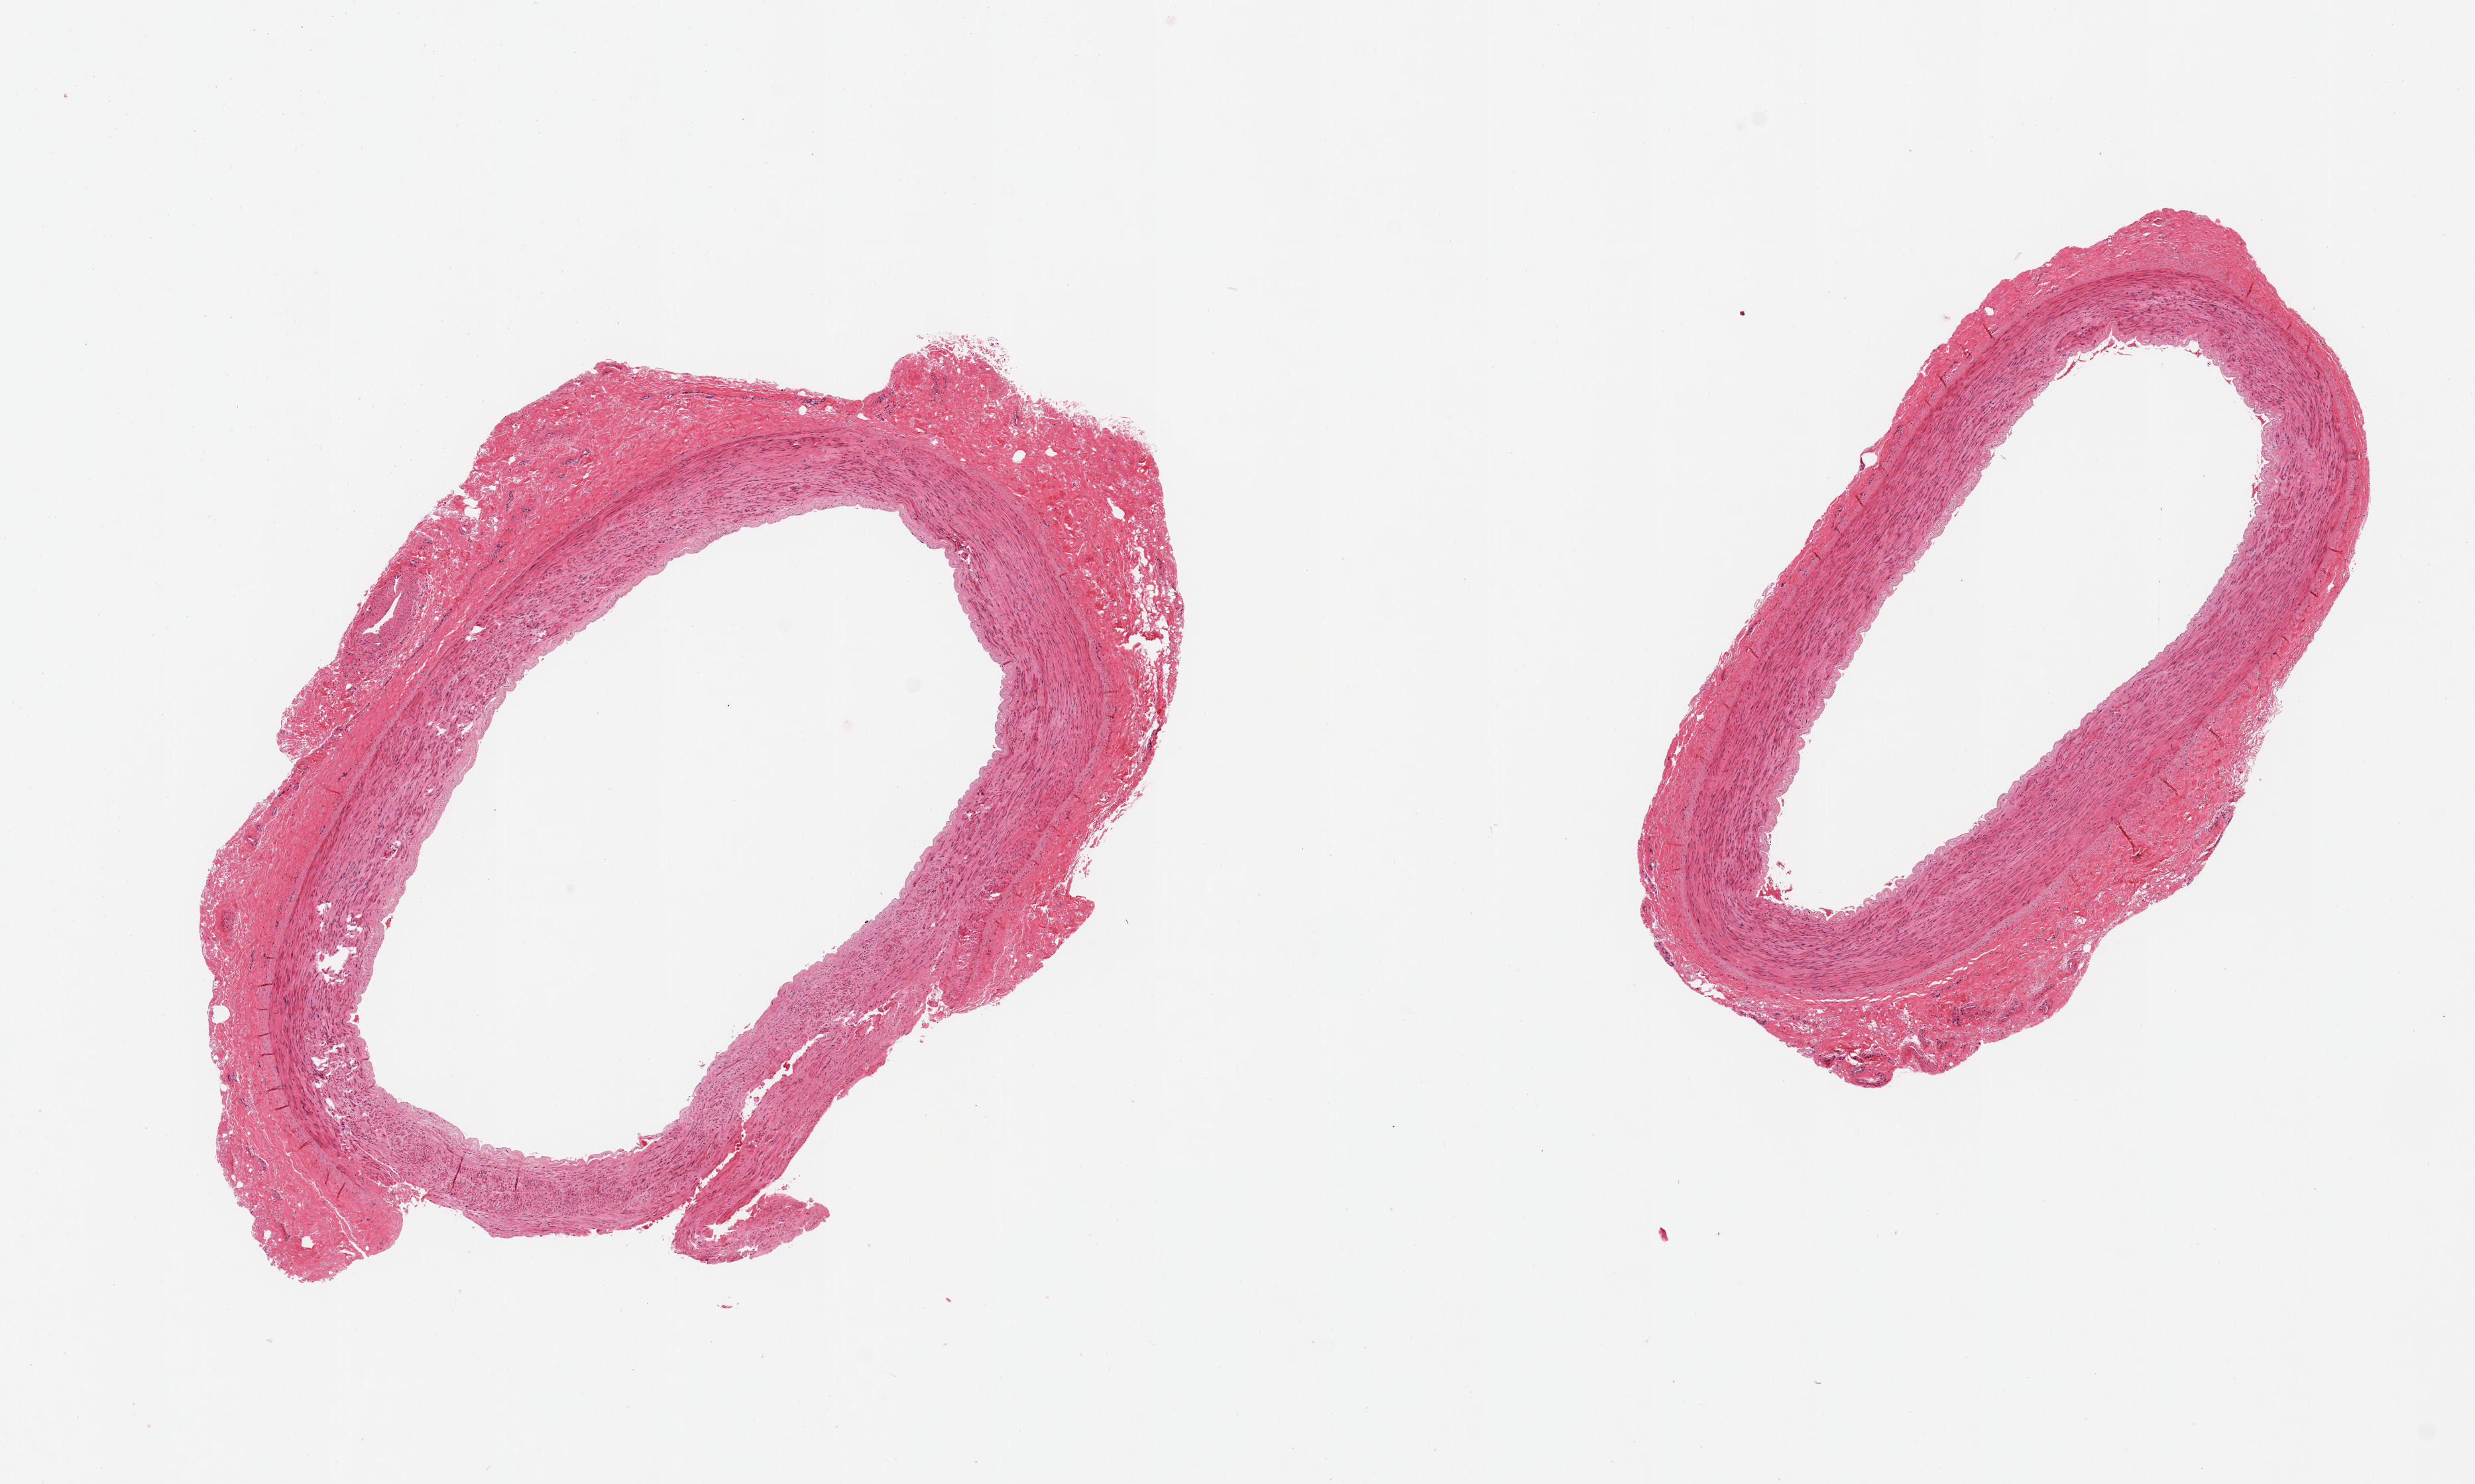
Digitized haematoxylin and eosin-stained section, a low-resolution overview of the entire scanned area, about 14.8 x 8.9 mm; PAXgene-fixed, paraffin-embedded tissue; target tissue: tibial artery; tissue donor sample. Donor sex: female.
* review note (as recorded): 2 pieces; well trimmed; no plaque